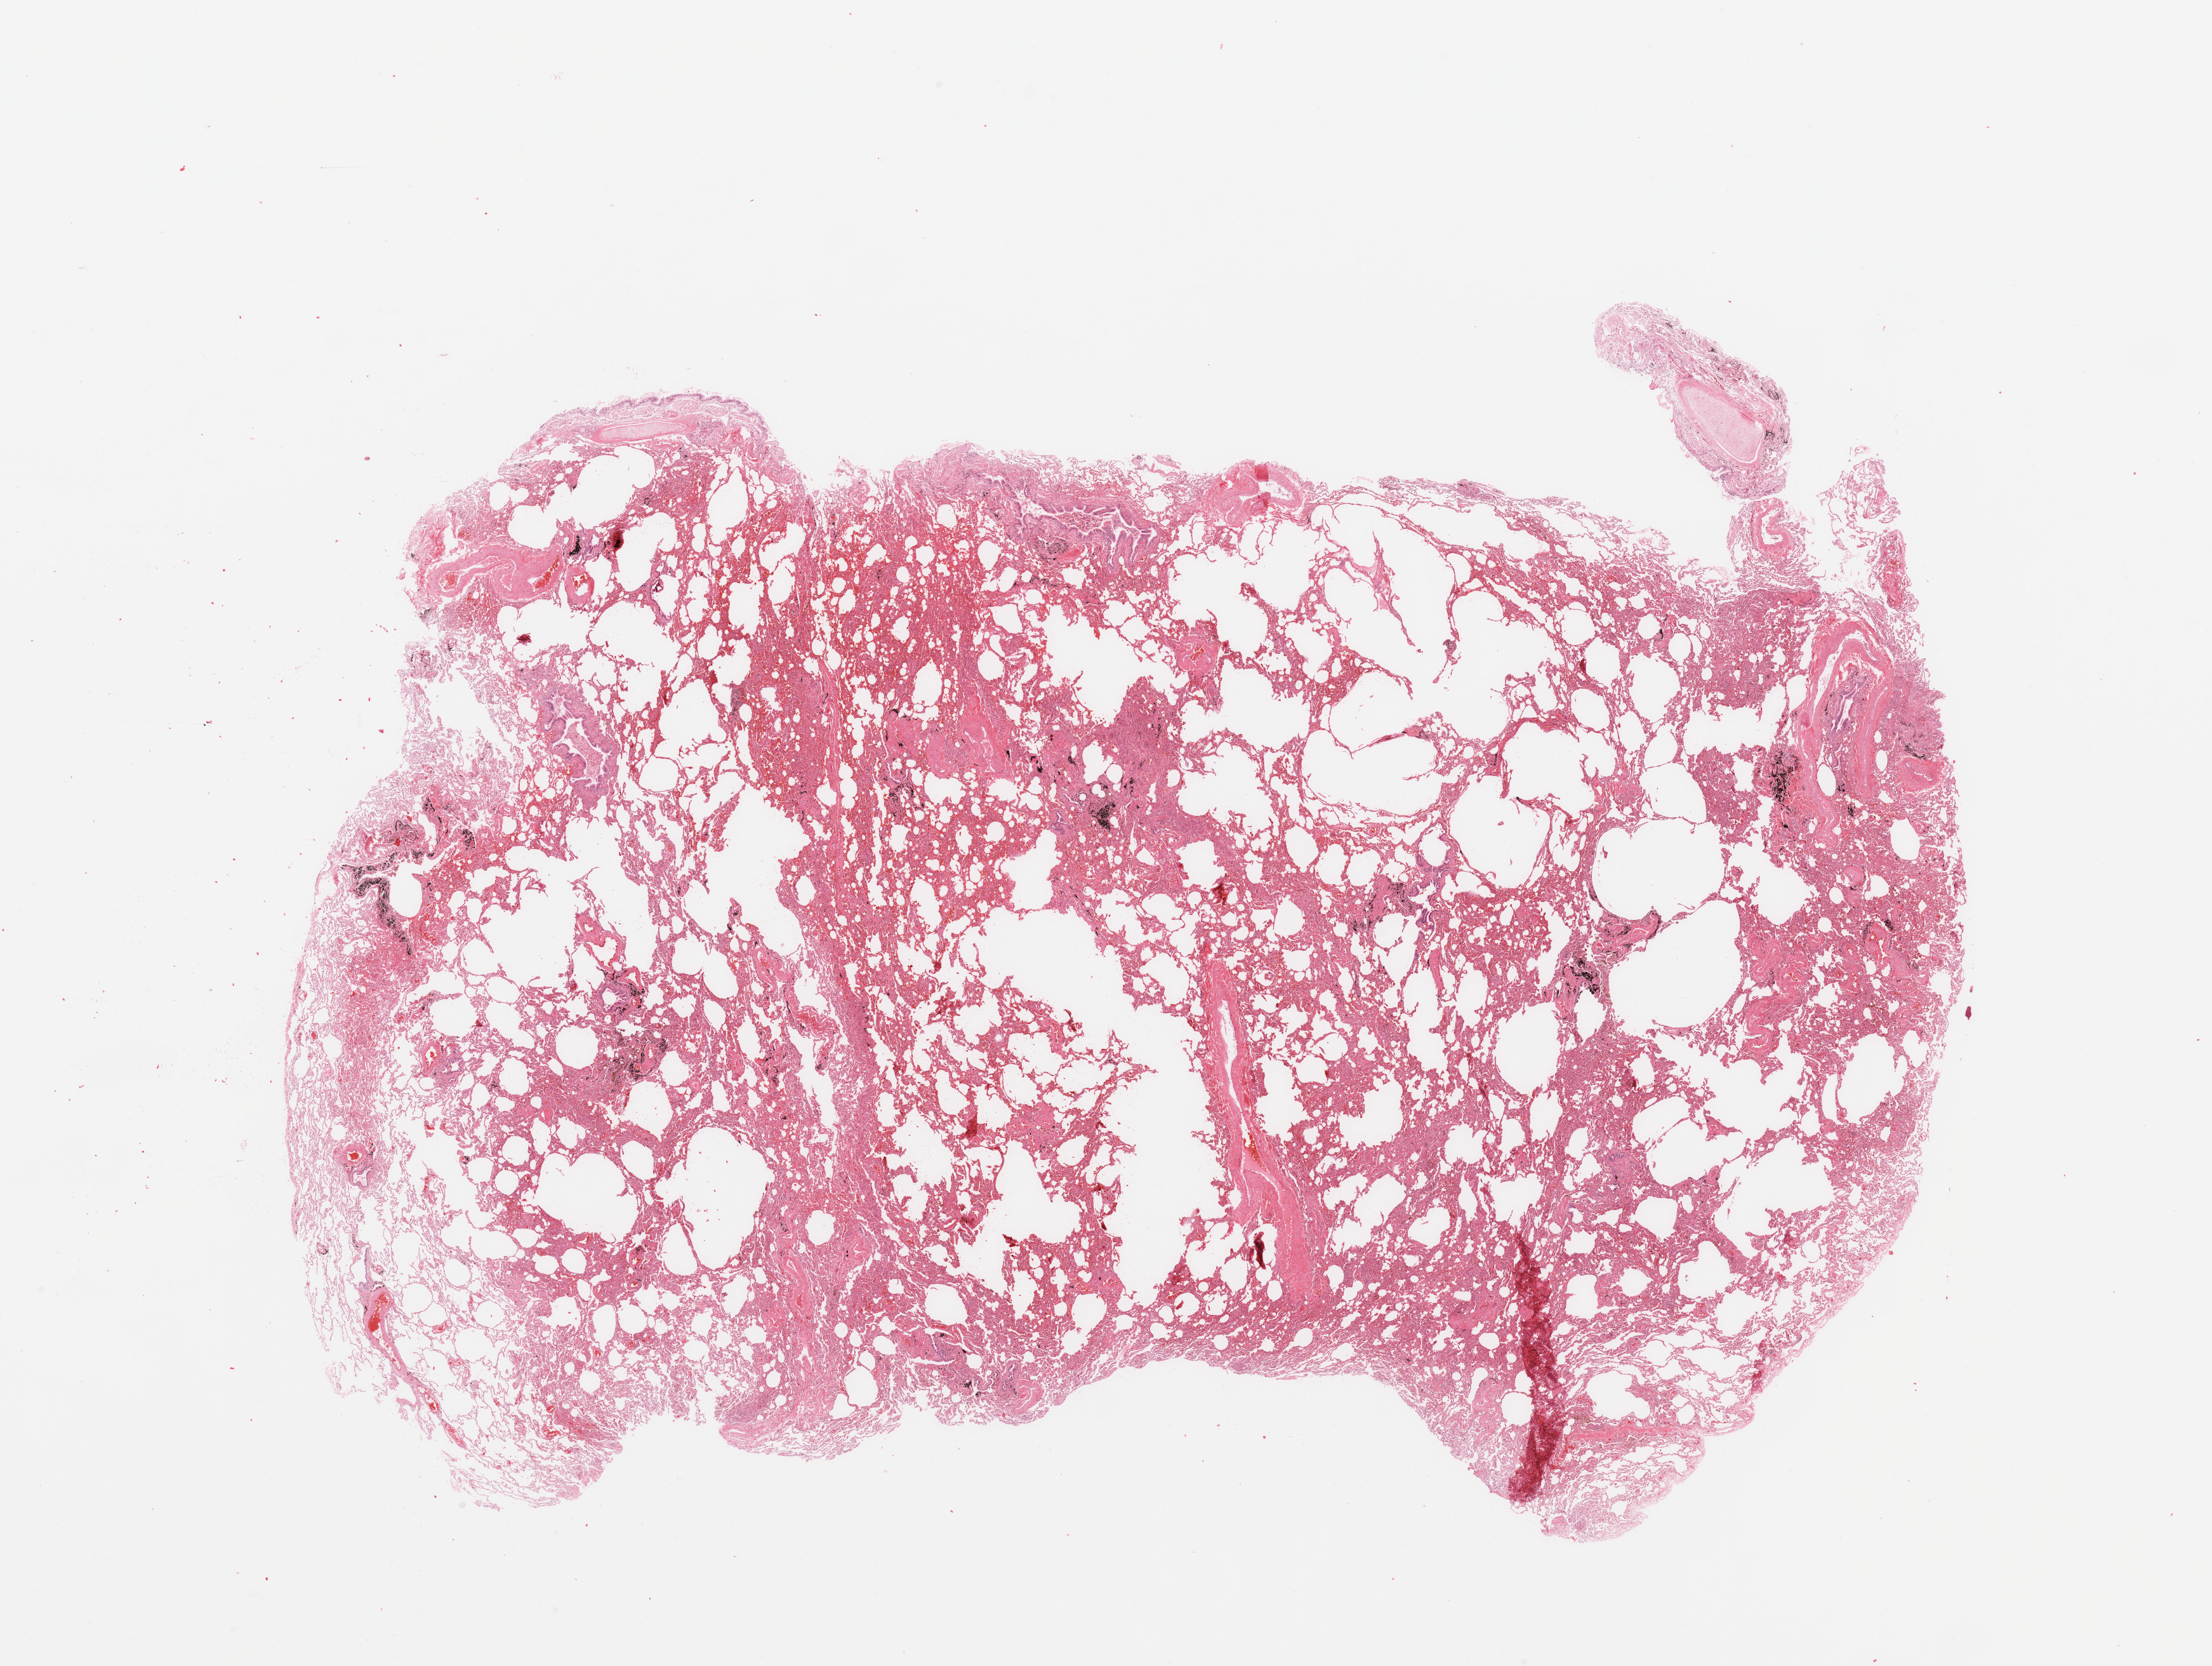
H&E-stained whole-slide image, low-resolution overview of the scanned area, about 27.6 x 20.8 mm (slide scanned at 20x), normal (non-tumour) tissue sample, sampled site: lung. 58-year-old male patient.
- this section: normal (non-tumour) tissue from the same patient
- patient diagnosis: Adenocarcinoma, NOS